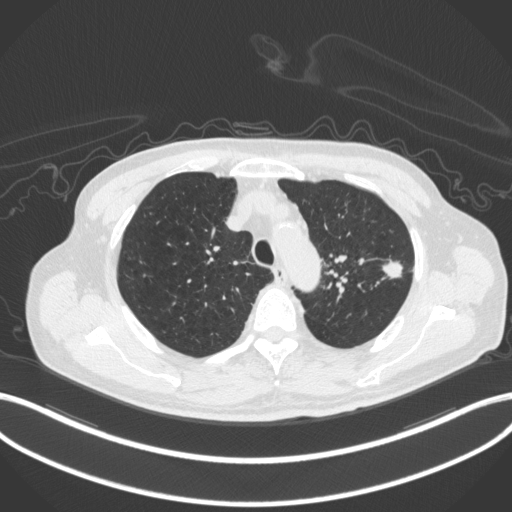
Chest CT, one axial slice. Lung window (W 1500 / L -600 HU). 1 mm slice thickness. 512 × 512 image matrix, field of view 400 × 400 mm. Patient: male, 77 years. From the clinical record (not read from this slice): clinical TNM (as recorded): T3 N1 M0.
Annotated regions visible in this slice (bounding box drawn by a radiologist):
- lung tumour (recorded histology: adenocarcinoma): bounding box (x1, y1, x2, y2) in pixels: (377, 257, 407, 282)